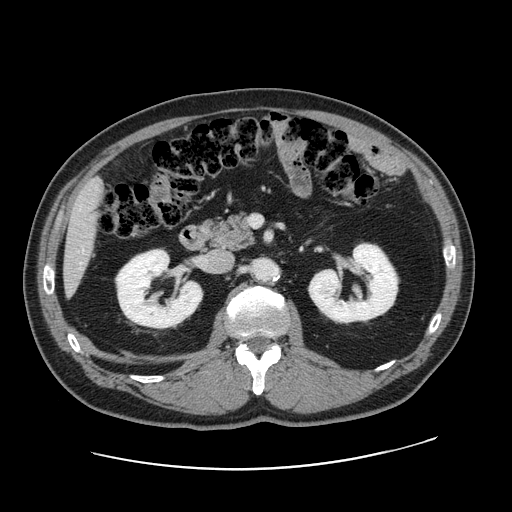
Contrast-enhanced abdominal CT, one axial slice. Position 74 of 178 along the scan axis. 120 kVp. Soft-tissue window (W 400 / L 40 HU). 2.5 mm slice thickness. 512 × 512 image matrix. Male patient, age 63 years. From the clinical record (not read from this slice): diagnosis: colorectal cancer liver metastases, imaged before liver resection; multiple liver metastases: yes; largest metastasis: 8 cm; disease in both lobes: yes.
Structures marked on this image (expert manual segmentation):
- liver: box from (x=64, y=180) to (x=102, y=291) px